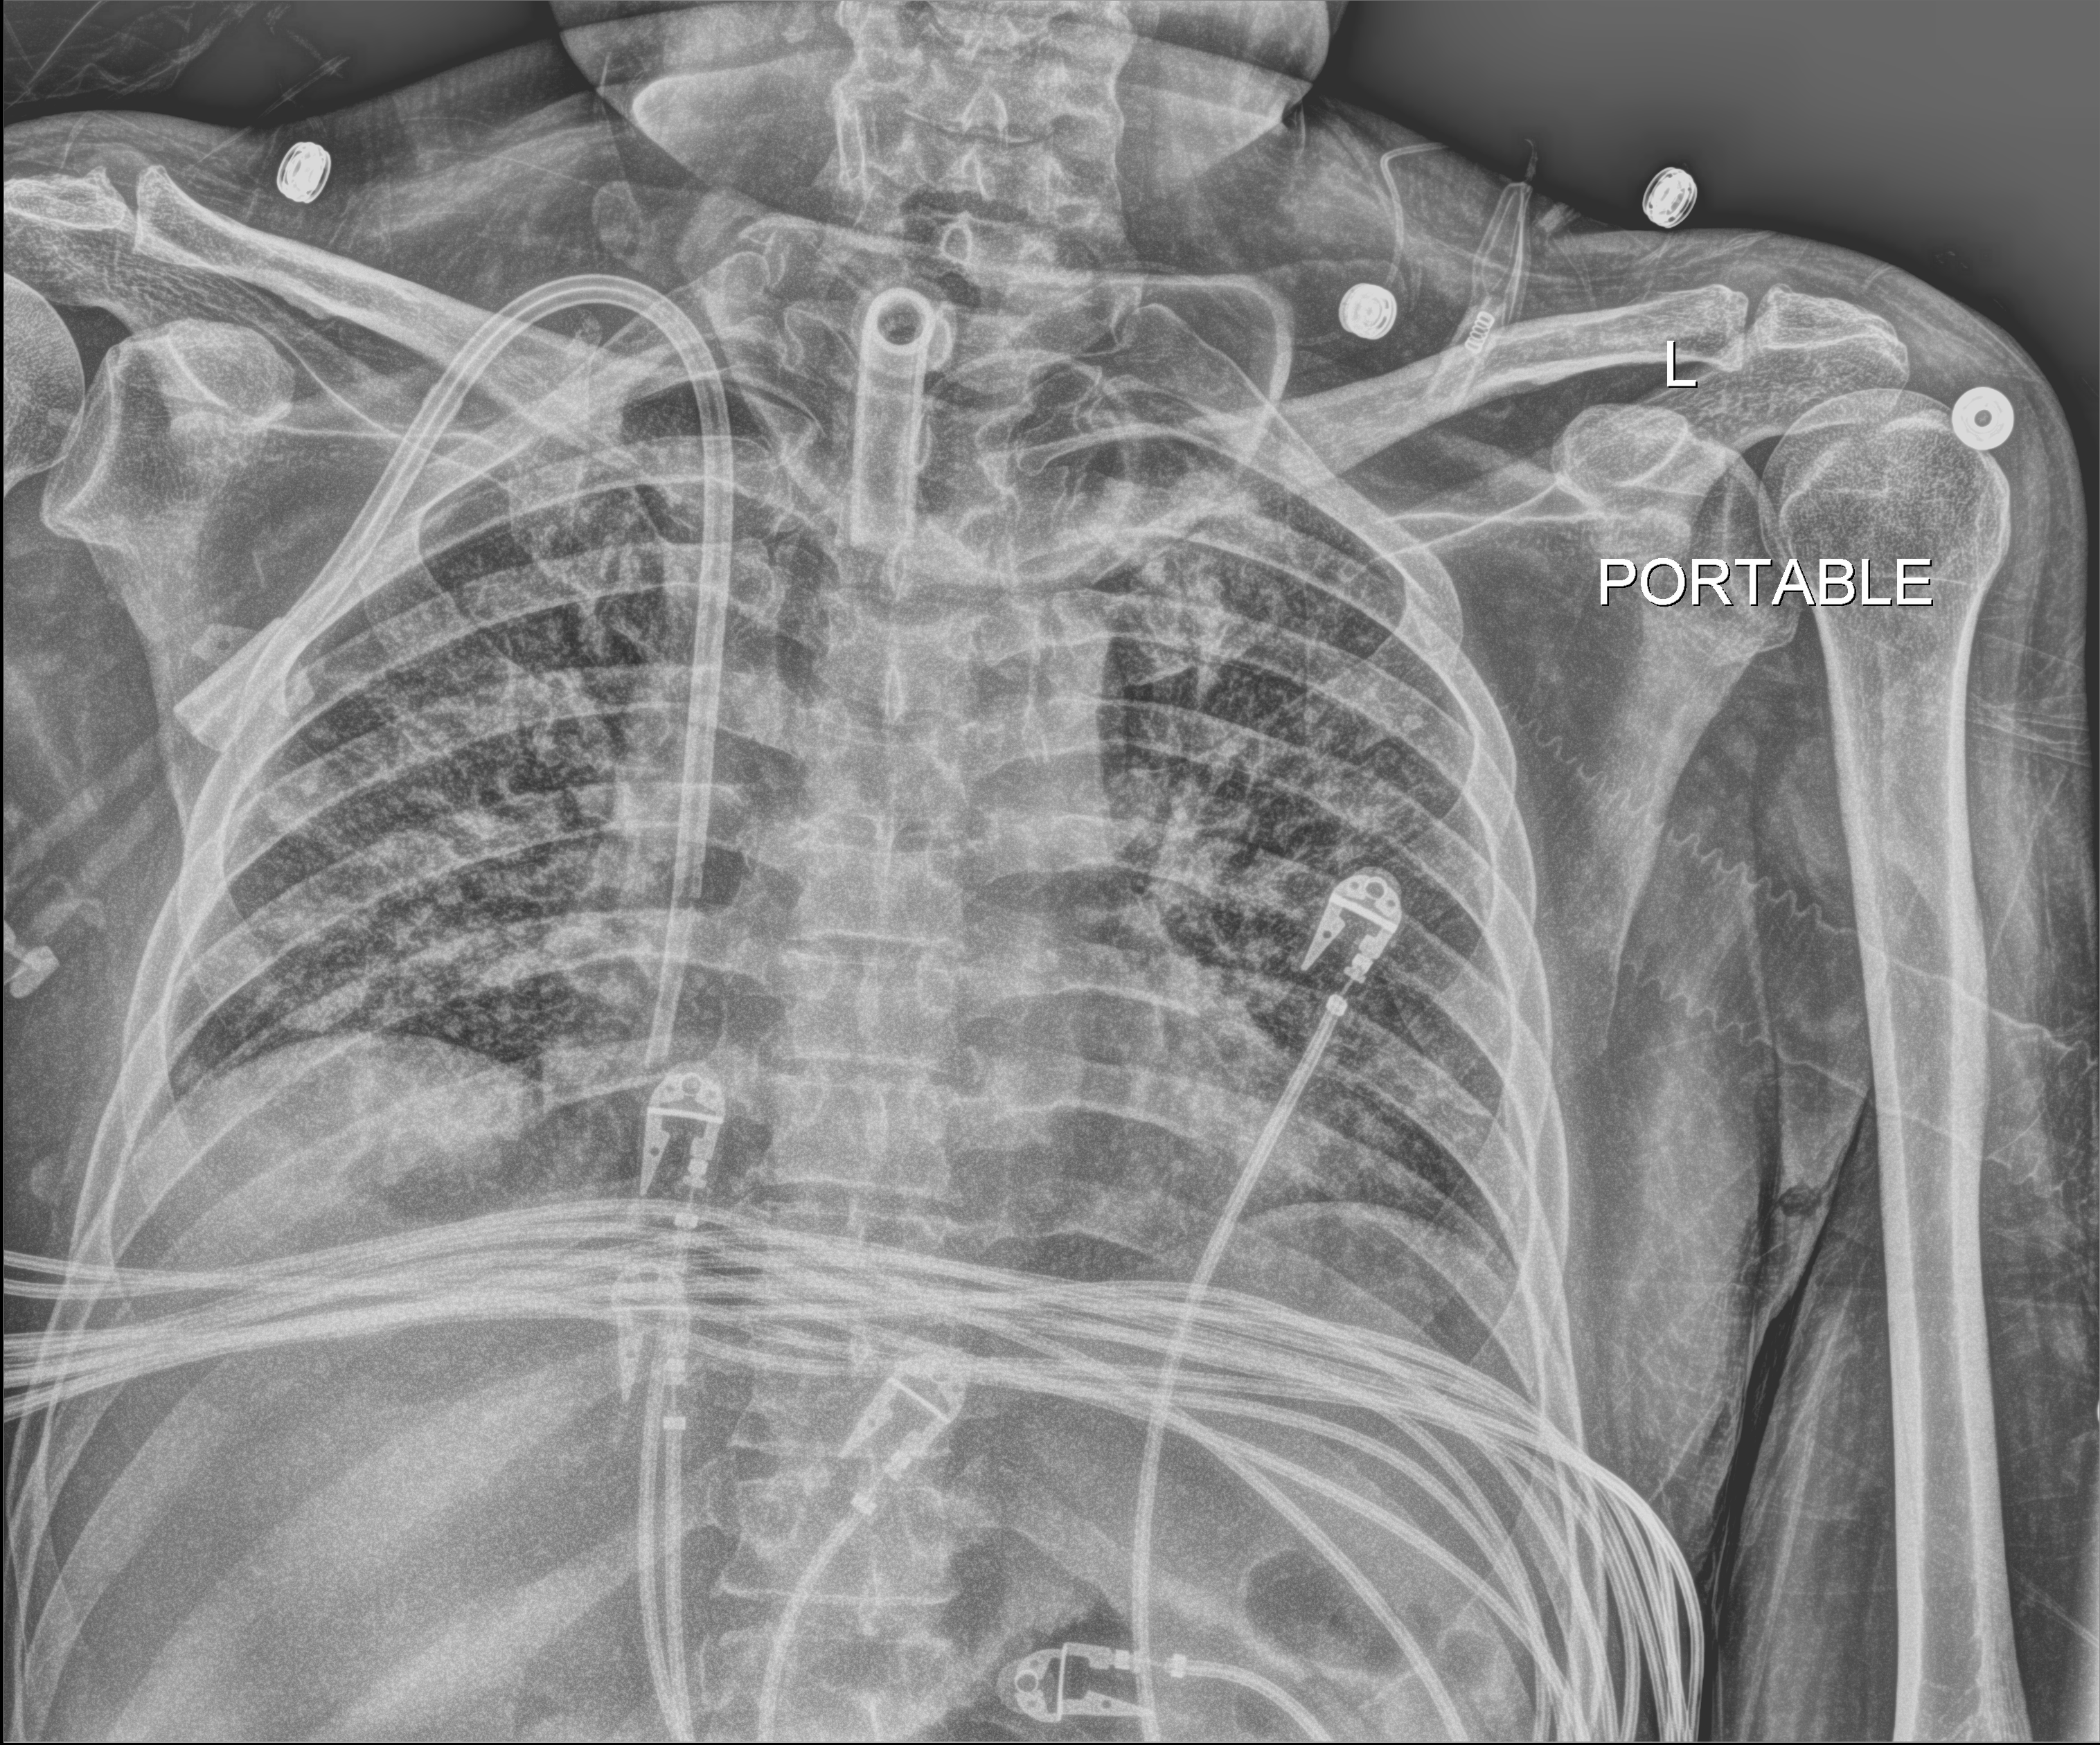
Chest X-ray (portable). Male patient hospitalised with COVID-19, age 18–59 years.
From the hospital-stay record, not from the radiograph (when in the stay this image was taken is not recorded):
- length of hospital stay: 77 days
- COPD (admission record): no
- hypertension (admission record): no